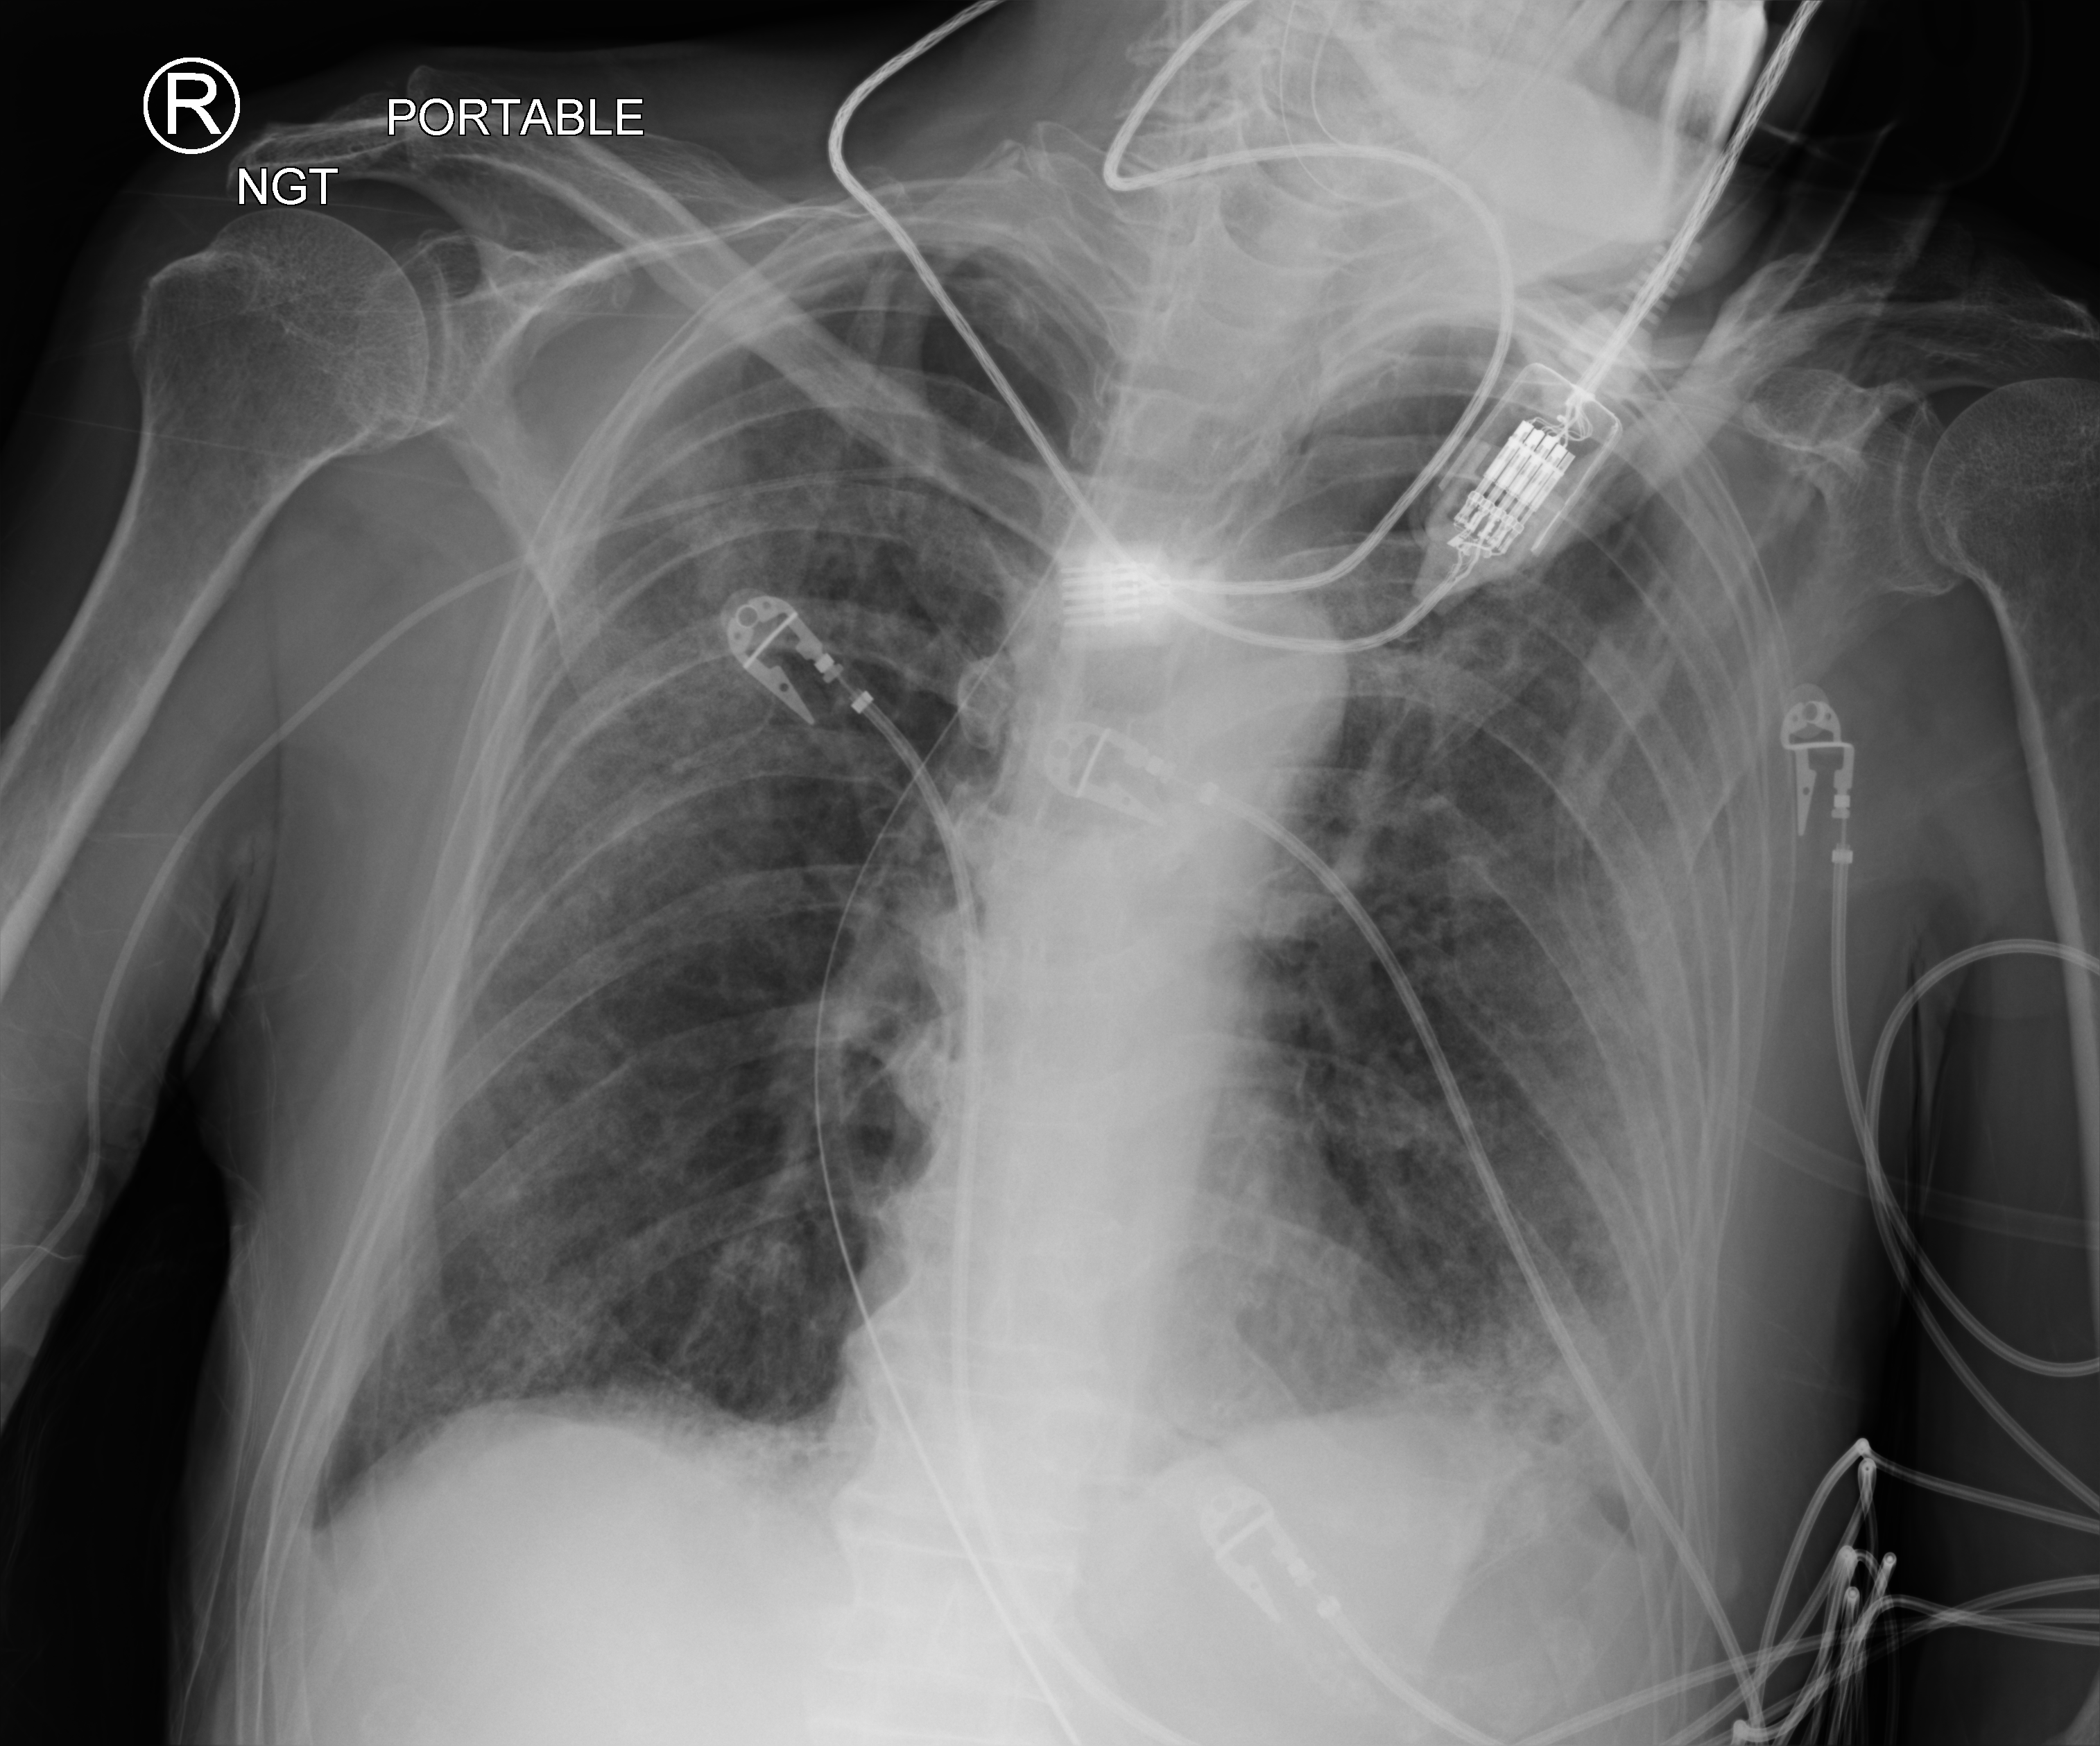
Portable chest radiograph; anteroposterior (AP) projection. Patient hospitalised with COVID-19; male, aged 60–74 years.
Admission-level facts for this patient (not findings on this image; timing relative to this image not recorded):
- diabetes (admission record): yes